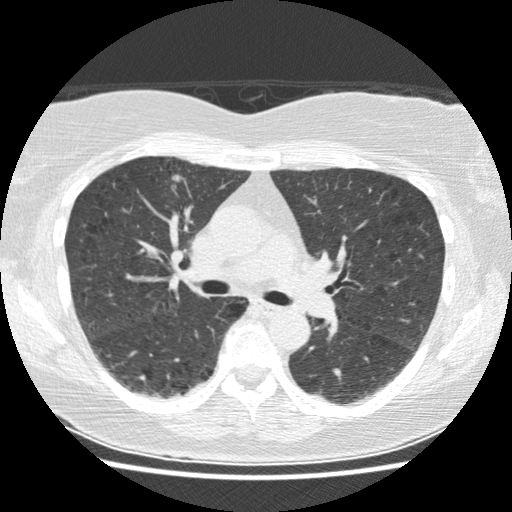
Axial slice from a low-dose chest CT screening exam; first (baseline) screen; lung window (W 1500 / L -600 HU); 2.5 mm slice thickness; standard (soft-tissue) reconstruction kernel (STANDARD); 120 kVp; slice 64 of 155 in the series; 512 × 512 image matrix, field of view 330 × 330 mm. Female, age 63 years at enrolment. Current smoker at enrolment.
• Lesion marked by an expert reader, bounding box <147,152,195,212> (left, top, right, bottom; pixels).
• The exam's reader record, not a measurement of the box and not confirmed to be the same lesion: non-calcified nodule or mass ≥4 mm, right upper lobe, 18 × 14 mm, spiculated (stellate) margins, soft tissue attenuation.
• Lung cancer was diagnosed 87 days after this screen: papillary adenocarcinoma, NOS, right upper lobe, well differentiated (G1), stage IA (AJCC 6th edition), 19 mm at pathology.